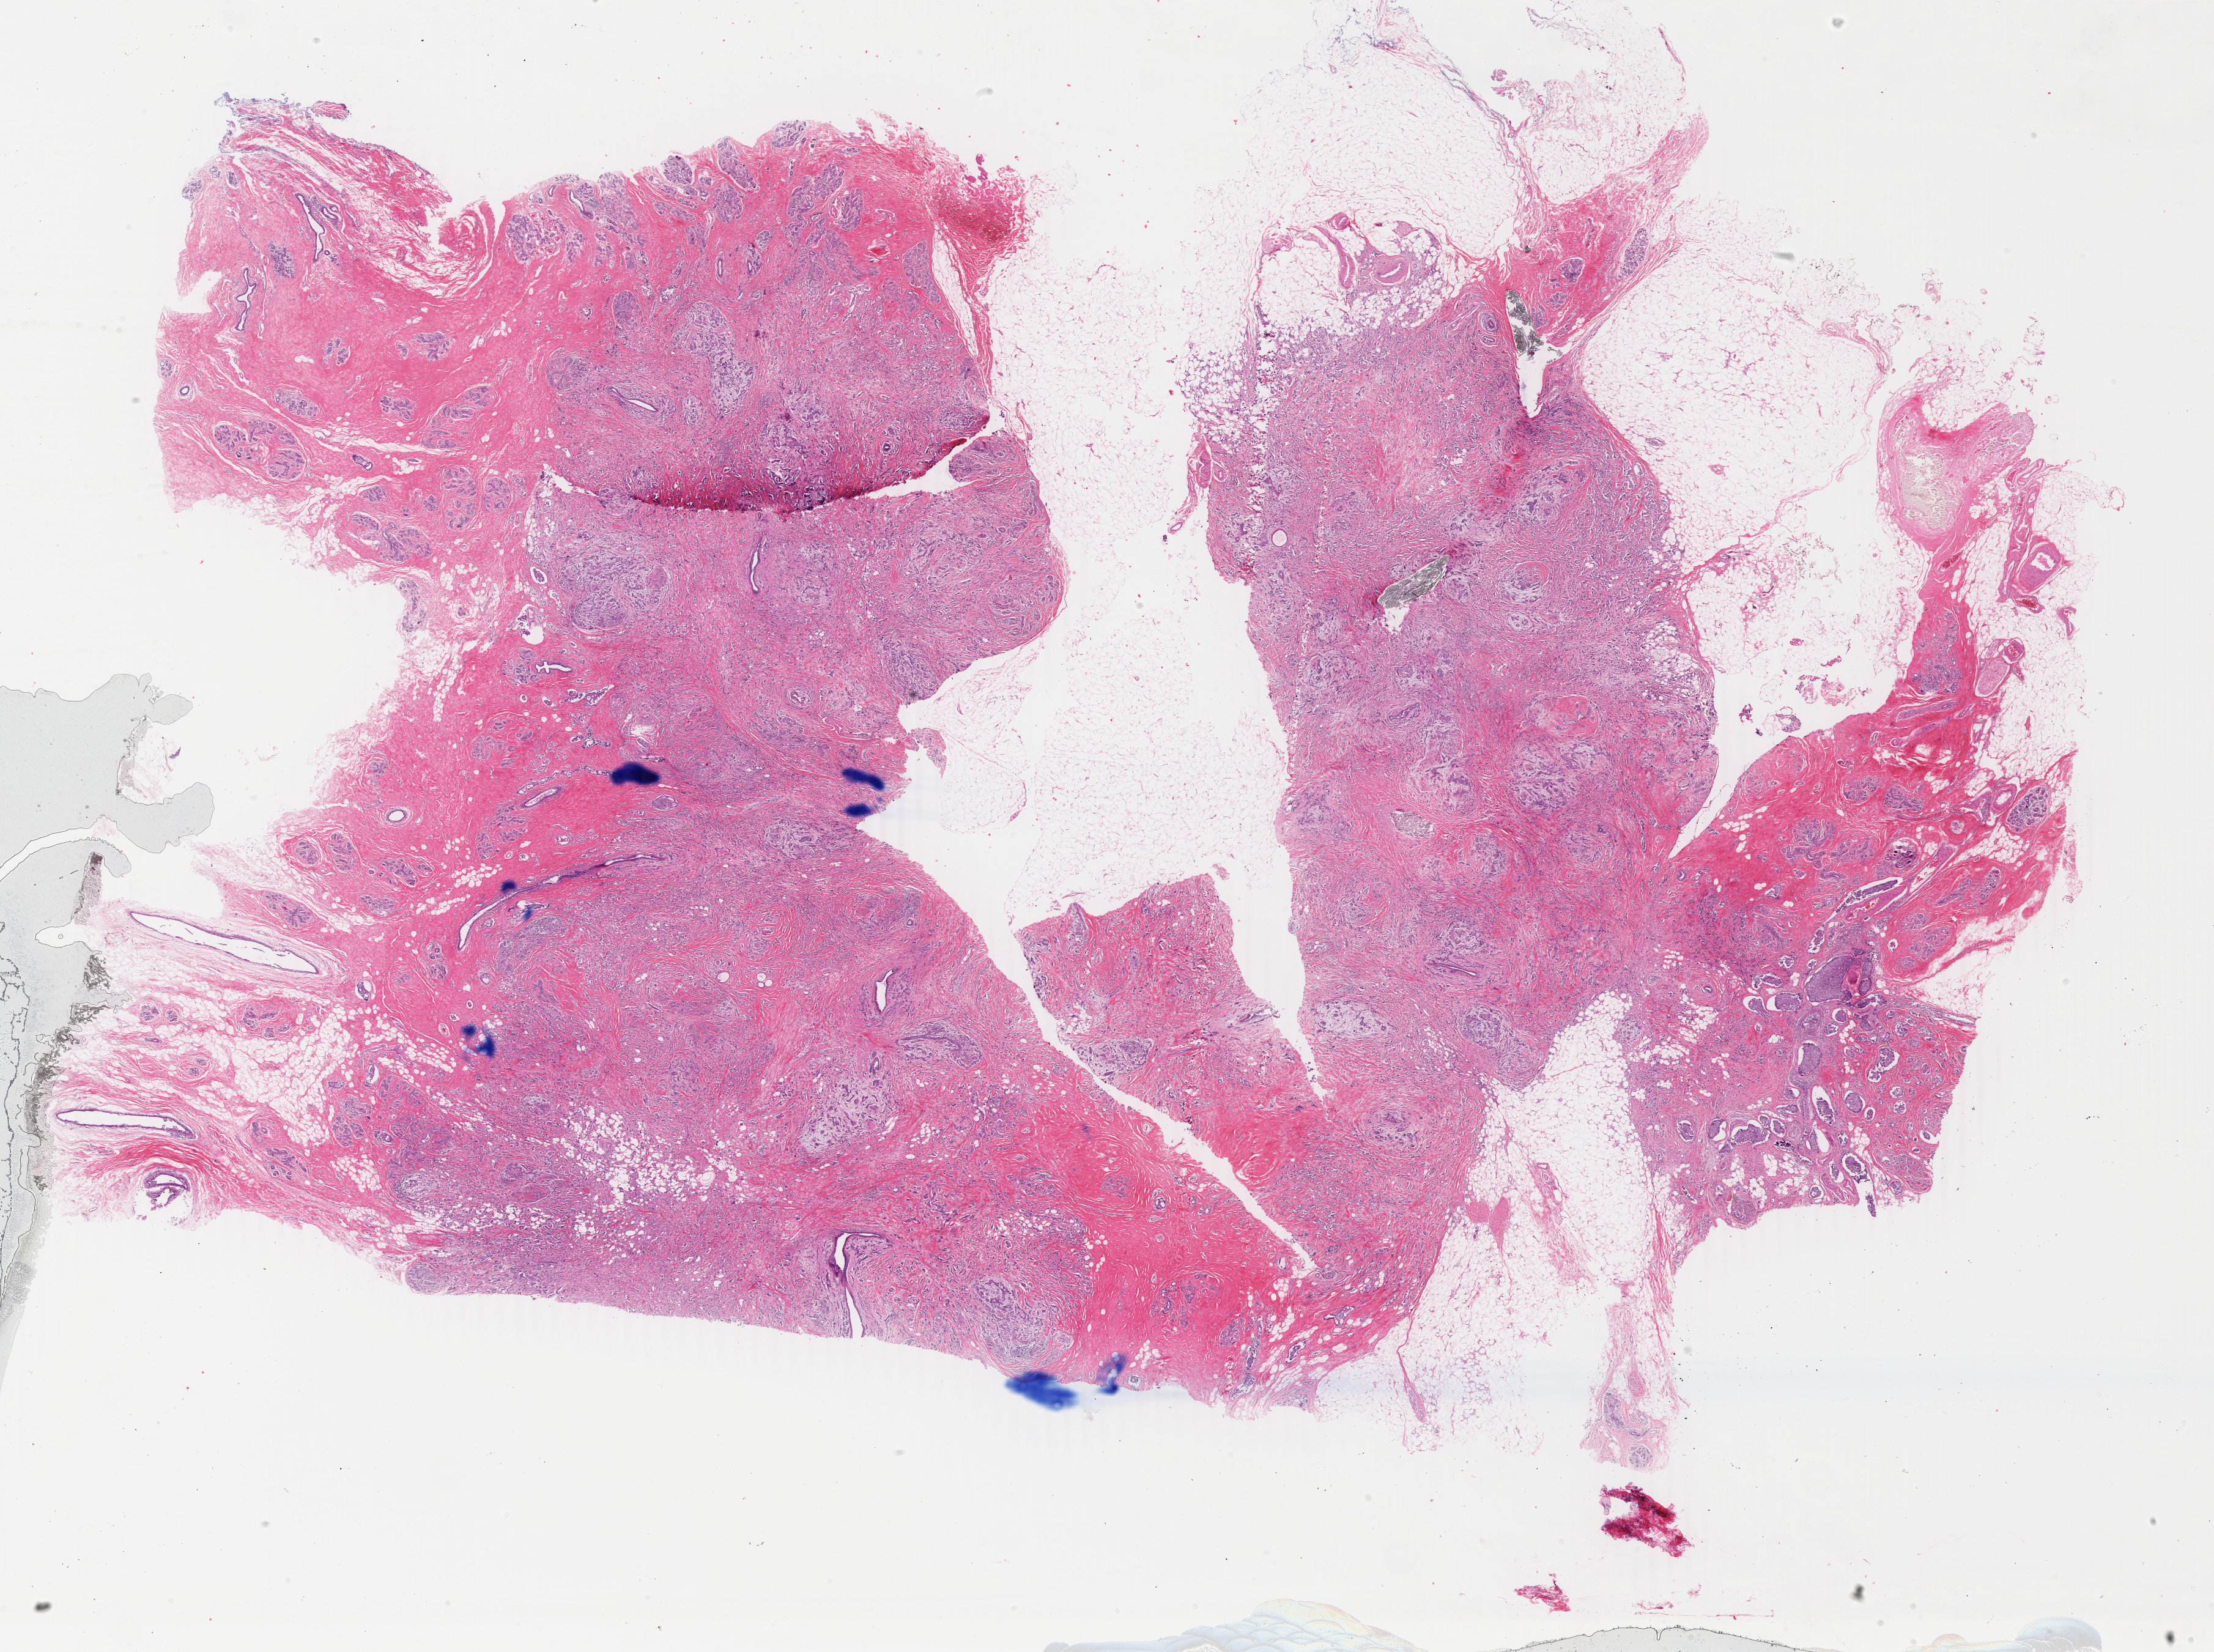
H&E-stained whole-slide image — low-resolution overview of the scanned area, about 28.8 x 21.5 mm. Formalin-fixed paraffin-embedded (FFPE) diagnostic section. Sample: primary tumour, breast. Female patient; age at initial diagnosis 40 years.
Diagnosis: Infiltrating duct carcinoma, NOS. Lymph nodes positive (case pathology): 3 of 21 examined. TNM: T3 N1b M0. AJCC pathologic stage: IIIA (4th edition).